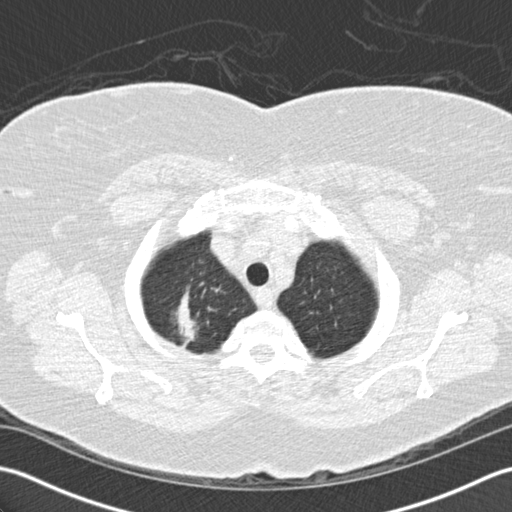
Chest CT (low-dose screening protocol), one axial image; baseline annual screen; lung window (W 1500 / L -600 HU); standard (soft-tissue) reconstruction kernel (B30f); slice 19 of 156 in the series; 512 × 512 image matrix, field of view 350 × 350 mm. Female participant, aged 72 years at enrolment.
Lesion marked by an expert reader, bounding box [x1, y1, x2, y2] px = [135, 277, 223, 367]. The screening reader recorded 2 non-calcified nodules or masses ≥4 mm on this exam (right lower lobe, right lower lobe); which of them this box marks is not recorded. Lung cancer was diagnosed 494 days after this screen: bronchiolo-alveolar adenocarcinoma, NOS, right upper lobe, stage IIIB (AJCC 6th edition), 45 mm at pathology.